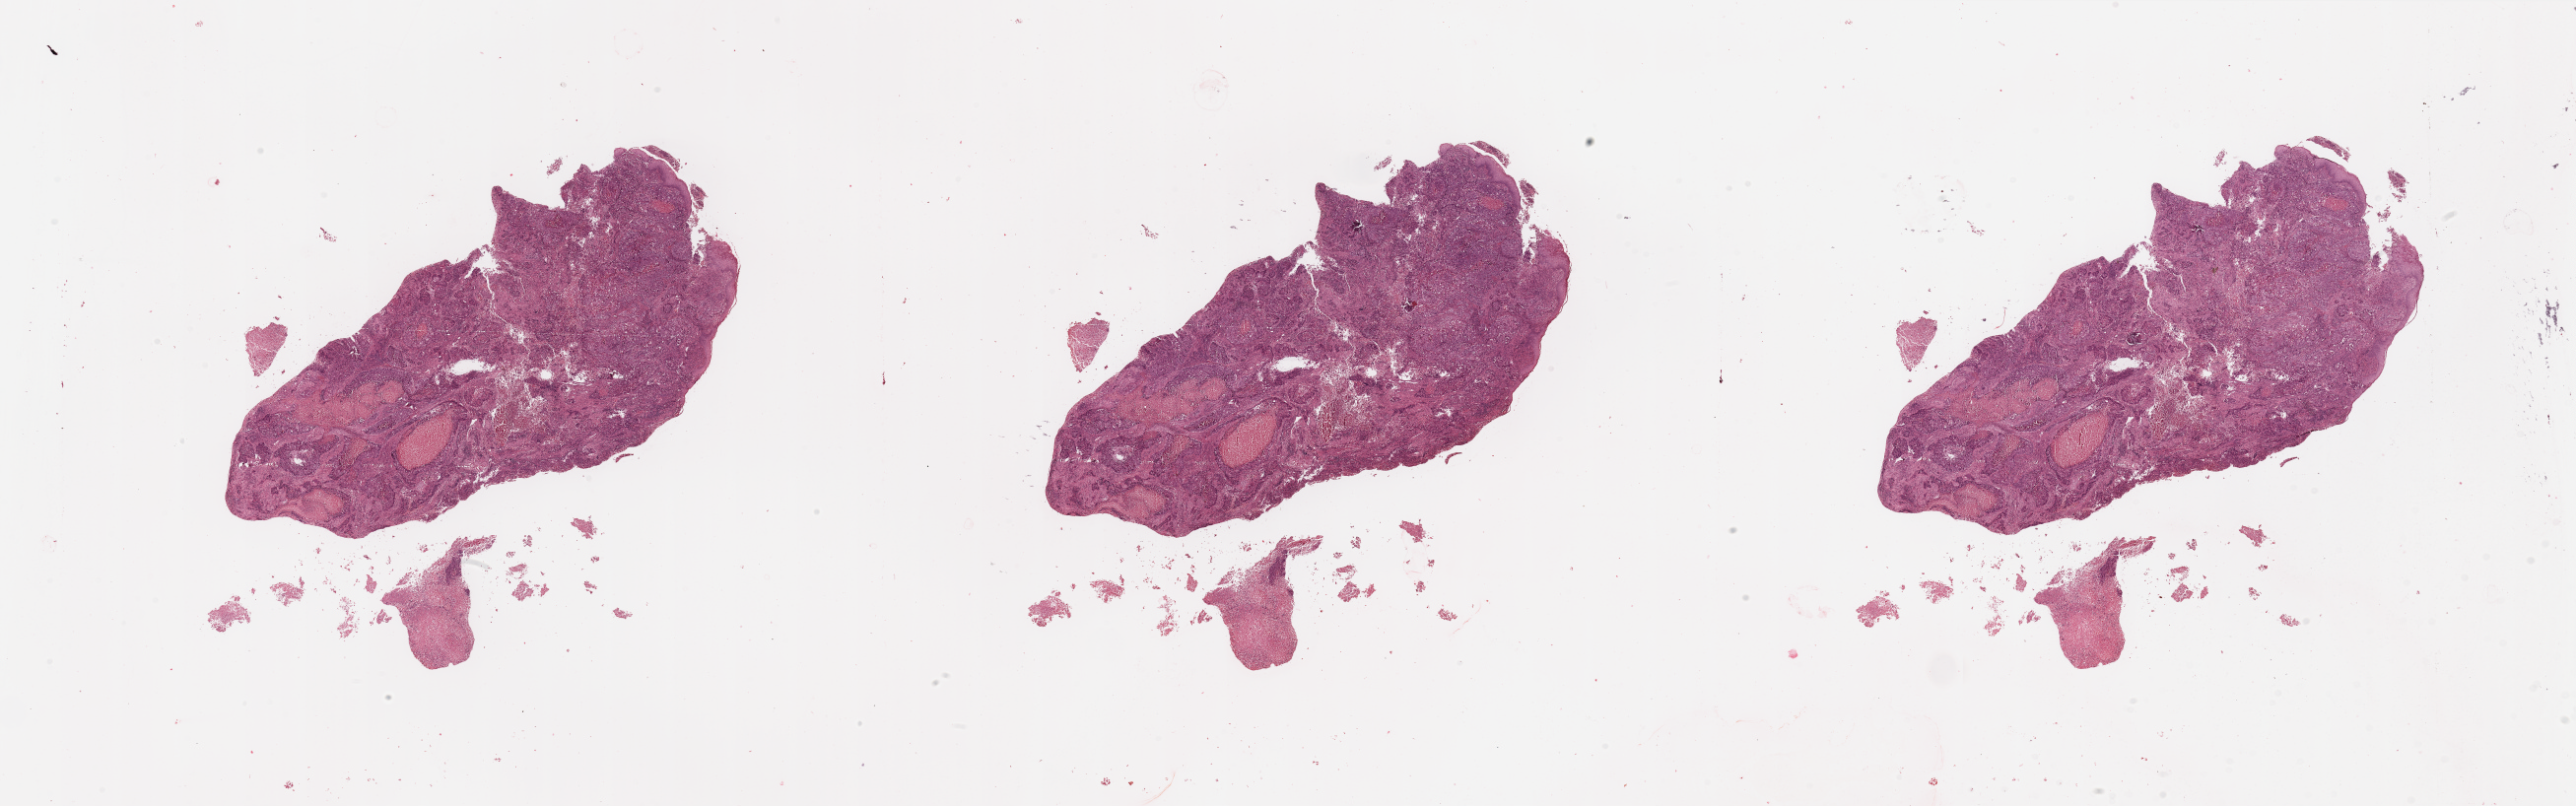
H&E-stained whole-slide image, shown as a low-resolution overview of the whole scanned area (about 41.3 x 12.9 mm, slide scanned at 20x), tumour tissue sample, sampled site: larynx. 64-year-old male patient. Histologic grade: G3 (poorly differentiated). Pathologist review of this section (percent, as recorded): tumour nuclei 85%, necrosis 15%.
- histologic diagnosis: Squamous cell carcinoma, NOS (larynx, NOS)
- primary tumour site (as recorded): larynx
- AJCC pathologic stage: II